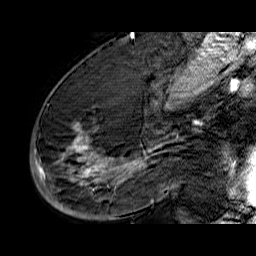
Breast MRI (dynamic contrast-enhanced), one sagittal slice. Slice 36 of 60 in the series (ordered by position). Dynamic contrast-enhanced series, time point 2 of 6 at this slice position (early post-contrast). 1.5 T. TE 6.5 ms, TR 32.9 ms. 4 mm slice thickness. 256 × 256 image matrix, field of view 200 × 200 mm. Female patient. Case-level facts recorded for this patient, not image findings: setting: breast cancer imaged before/during neoadjuvant chemotherapy; receptor status: HR-positive, HER2-negative.
Annotated regions visible in this slice (semi-automatic segmentation, software-assisted and operator-edited):
- analysis volume of interest (the breast-tissue region the enhancement analysis was run in; not a lesion): bounding box [x1, y1, x2, y2] px = [33, 74, 176, 210]
- tumour enhancement mask (voxels above the 100 % enhancement threshold inside the analysis volume of interest): [34, 87, 176, 191]